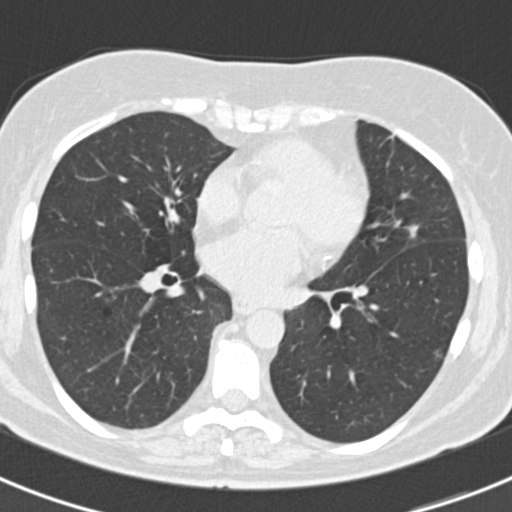
Low-dose screening chest CT, axial slice, baseline screening round, lung window (W 1500 / L -600 HU), slice 109 of 184 in the series, 512 × 512 image matrix, field of view 298 × 298 mm. Female, age 60 years at enrolment. Current smoker at enrolment.
- Expert-annotated lung lesion, bounding box [x1, y1, x2, y2] px = [397, 216, 432, 250].
- The screening reader recorded 3 non-calcified nodules or masses ≥4 mm on this exam (lingula, left lower lobe, lingula); which of them this box marks is not recorded.
- Official screen result: positive, change unspecified: nodule(s) >= 4 mm or enlarging nodule(s), mass(es), or other non-specific abnormalities suspicious for lung cancer.
- Lung cancer was diagnosed 886 days after this screen (after the third annual screen): non-small cell carcinoma, left upper lobe, poorly differentiated (G3), stage IB (AJCC 6th edition), 7 mm at pathology.